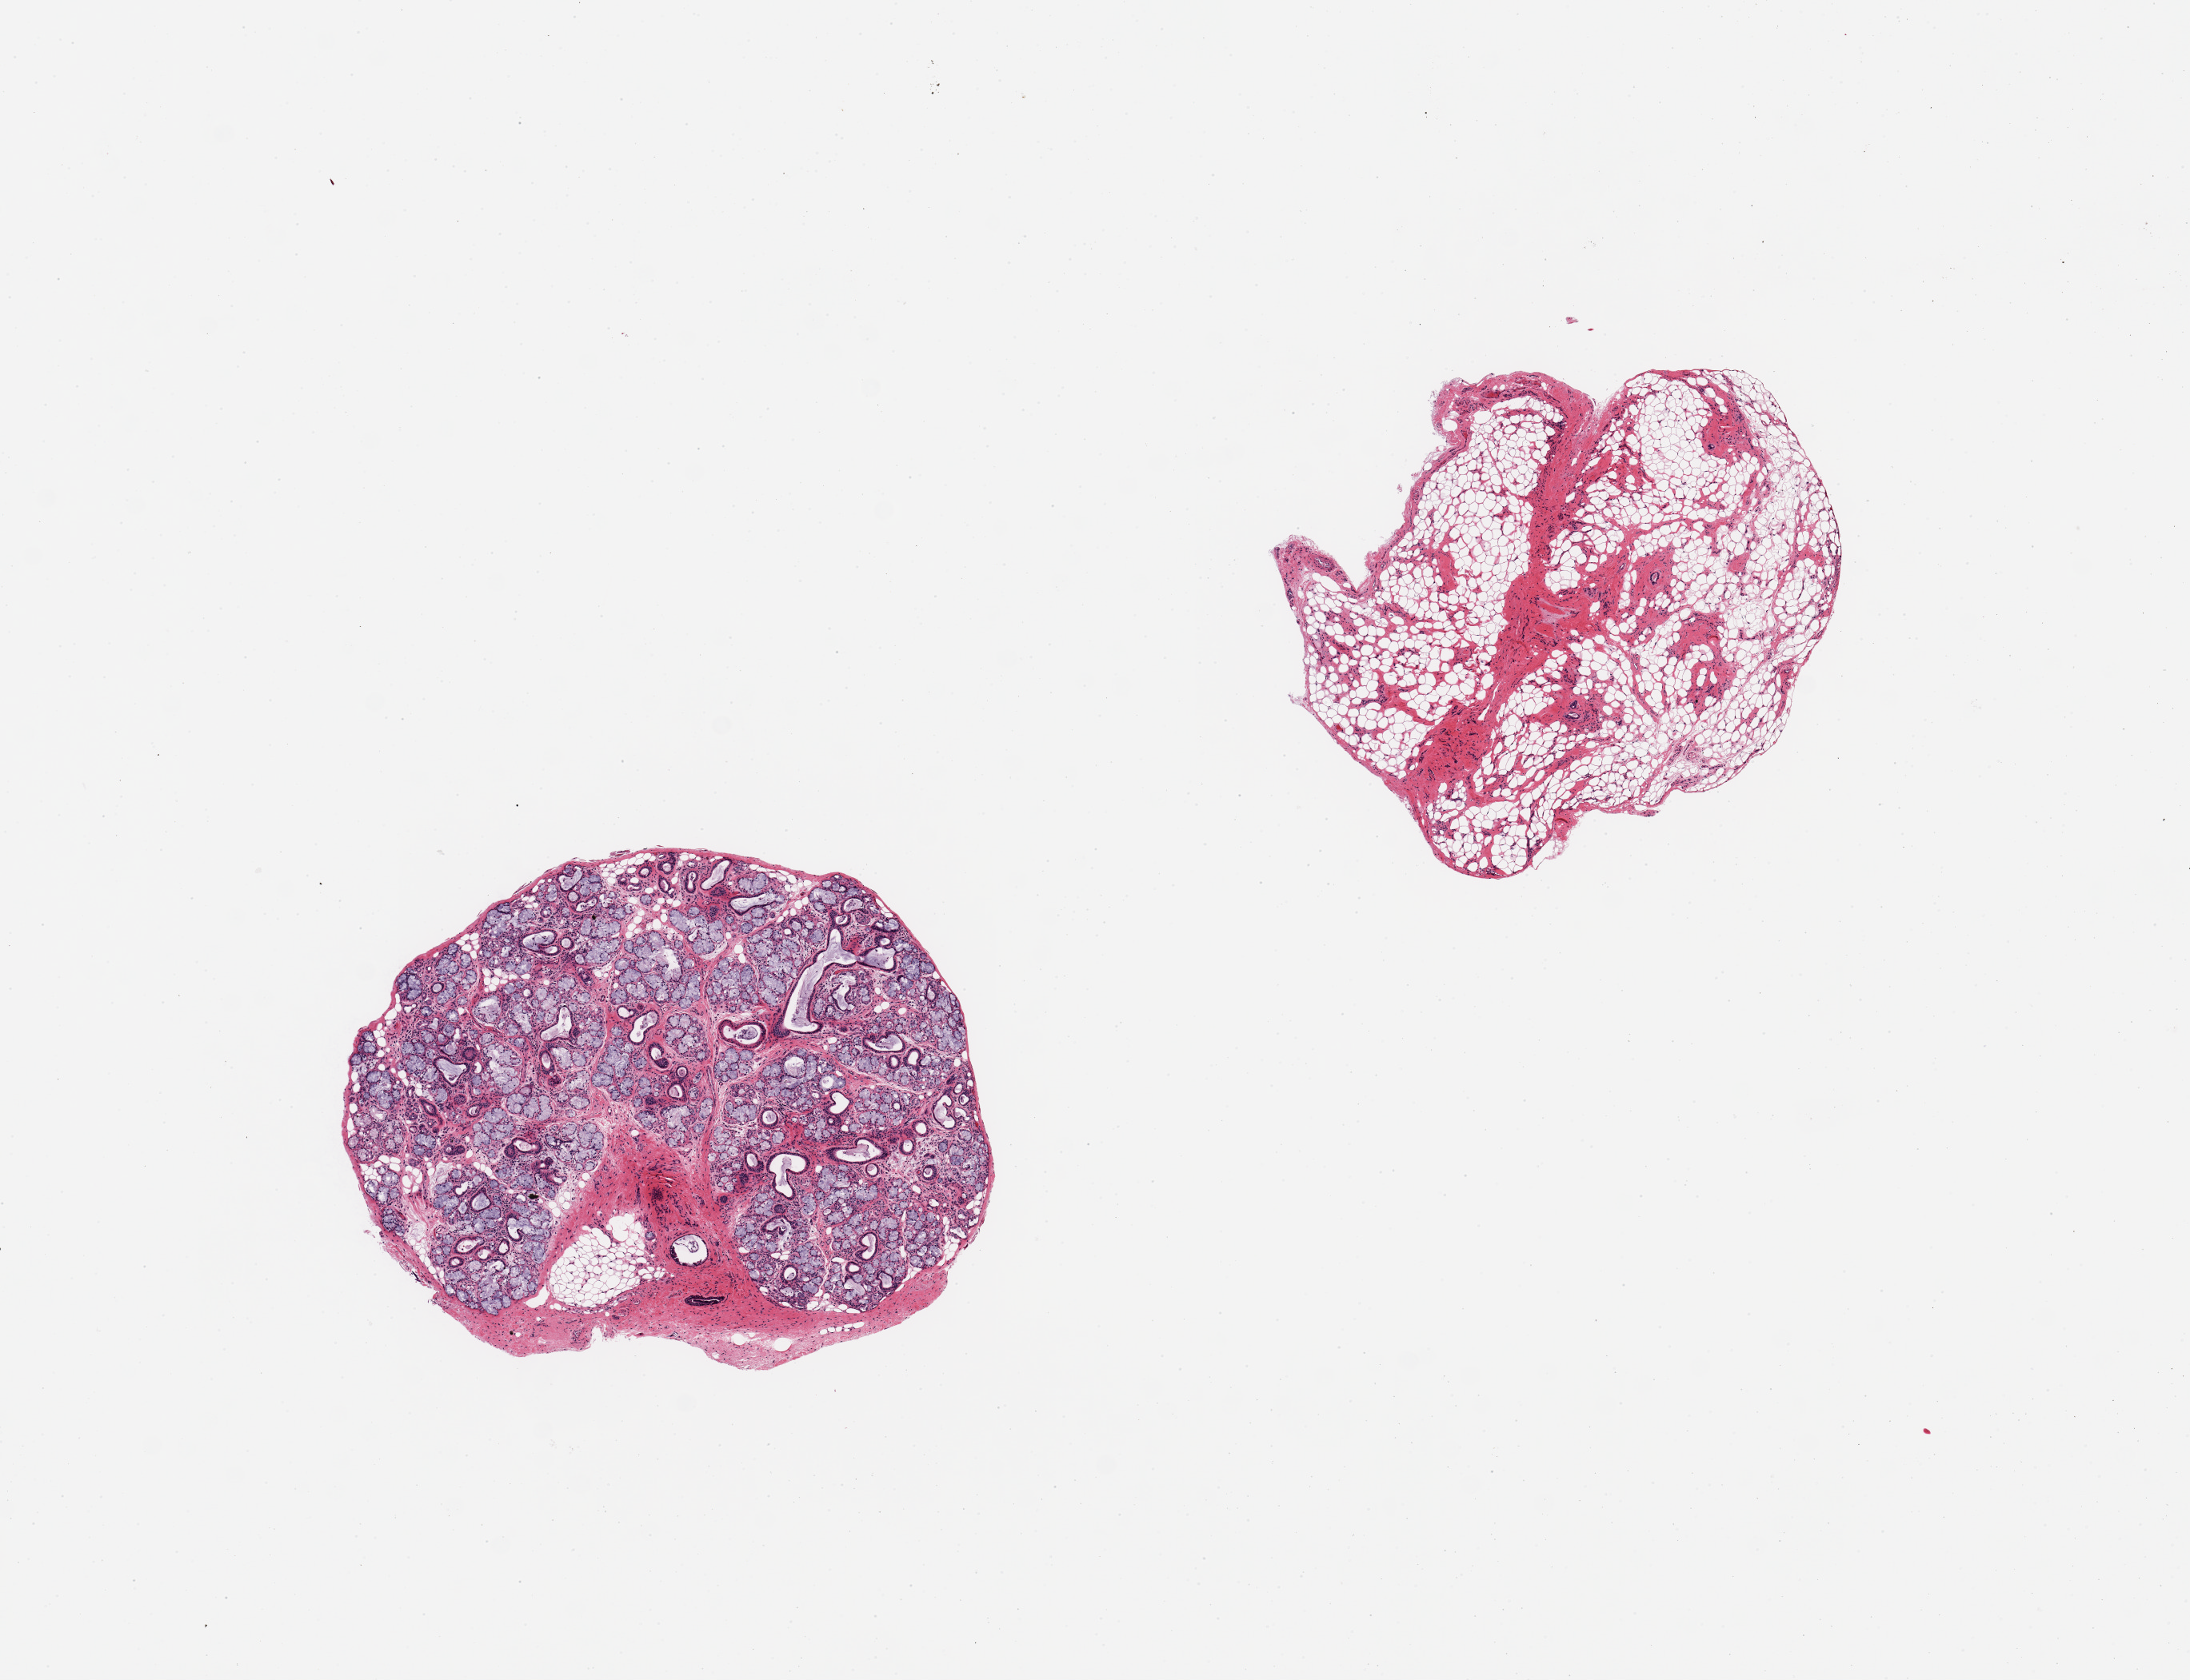
Digitized H&E-stained section — whole scanned area (about 10.8 x 8.3 mm, acquisition: 20x scan) shown as a low-resolution overview. PAXgene-fixed, paraffin-embedded tissue. Sampled site (target tissue): minor salivary gland. Donor tissue sample.
• pathologist's review note for this sample: 2 pieces; well trimmed salivary gland; second piece represents adipose tissue with fibrovascular component